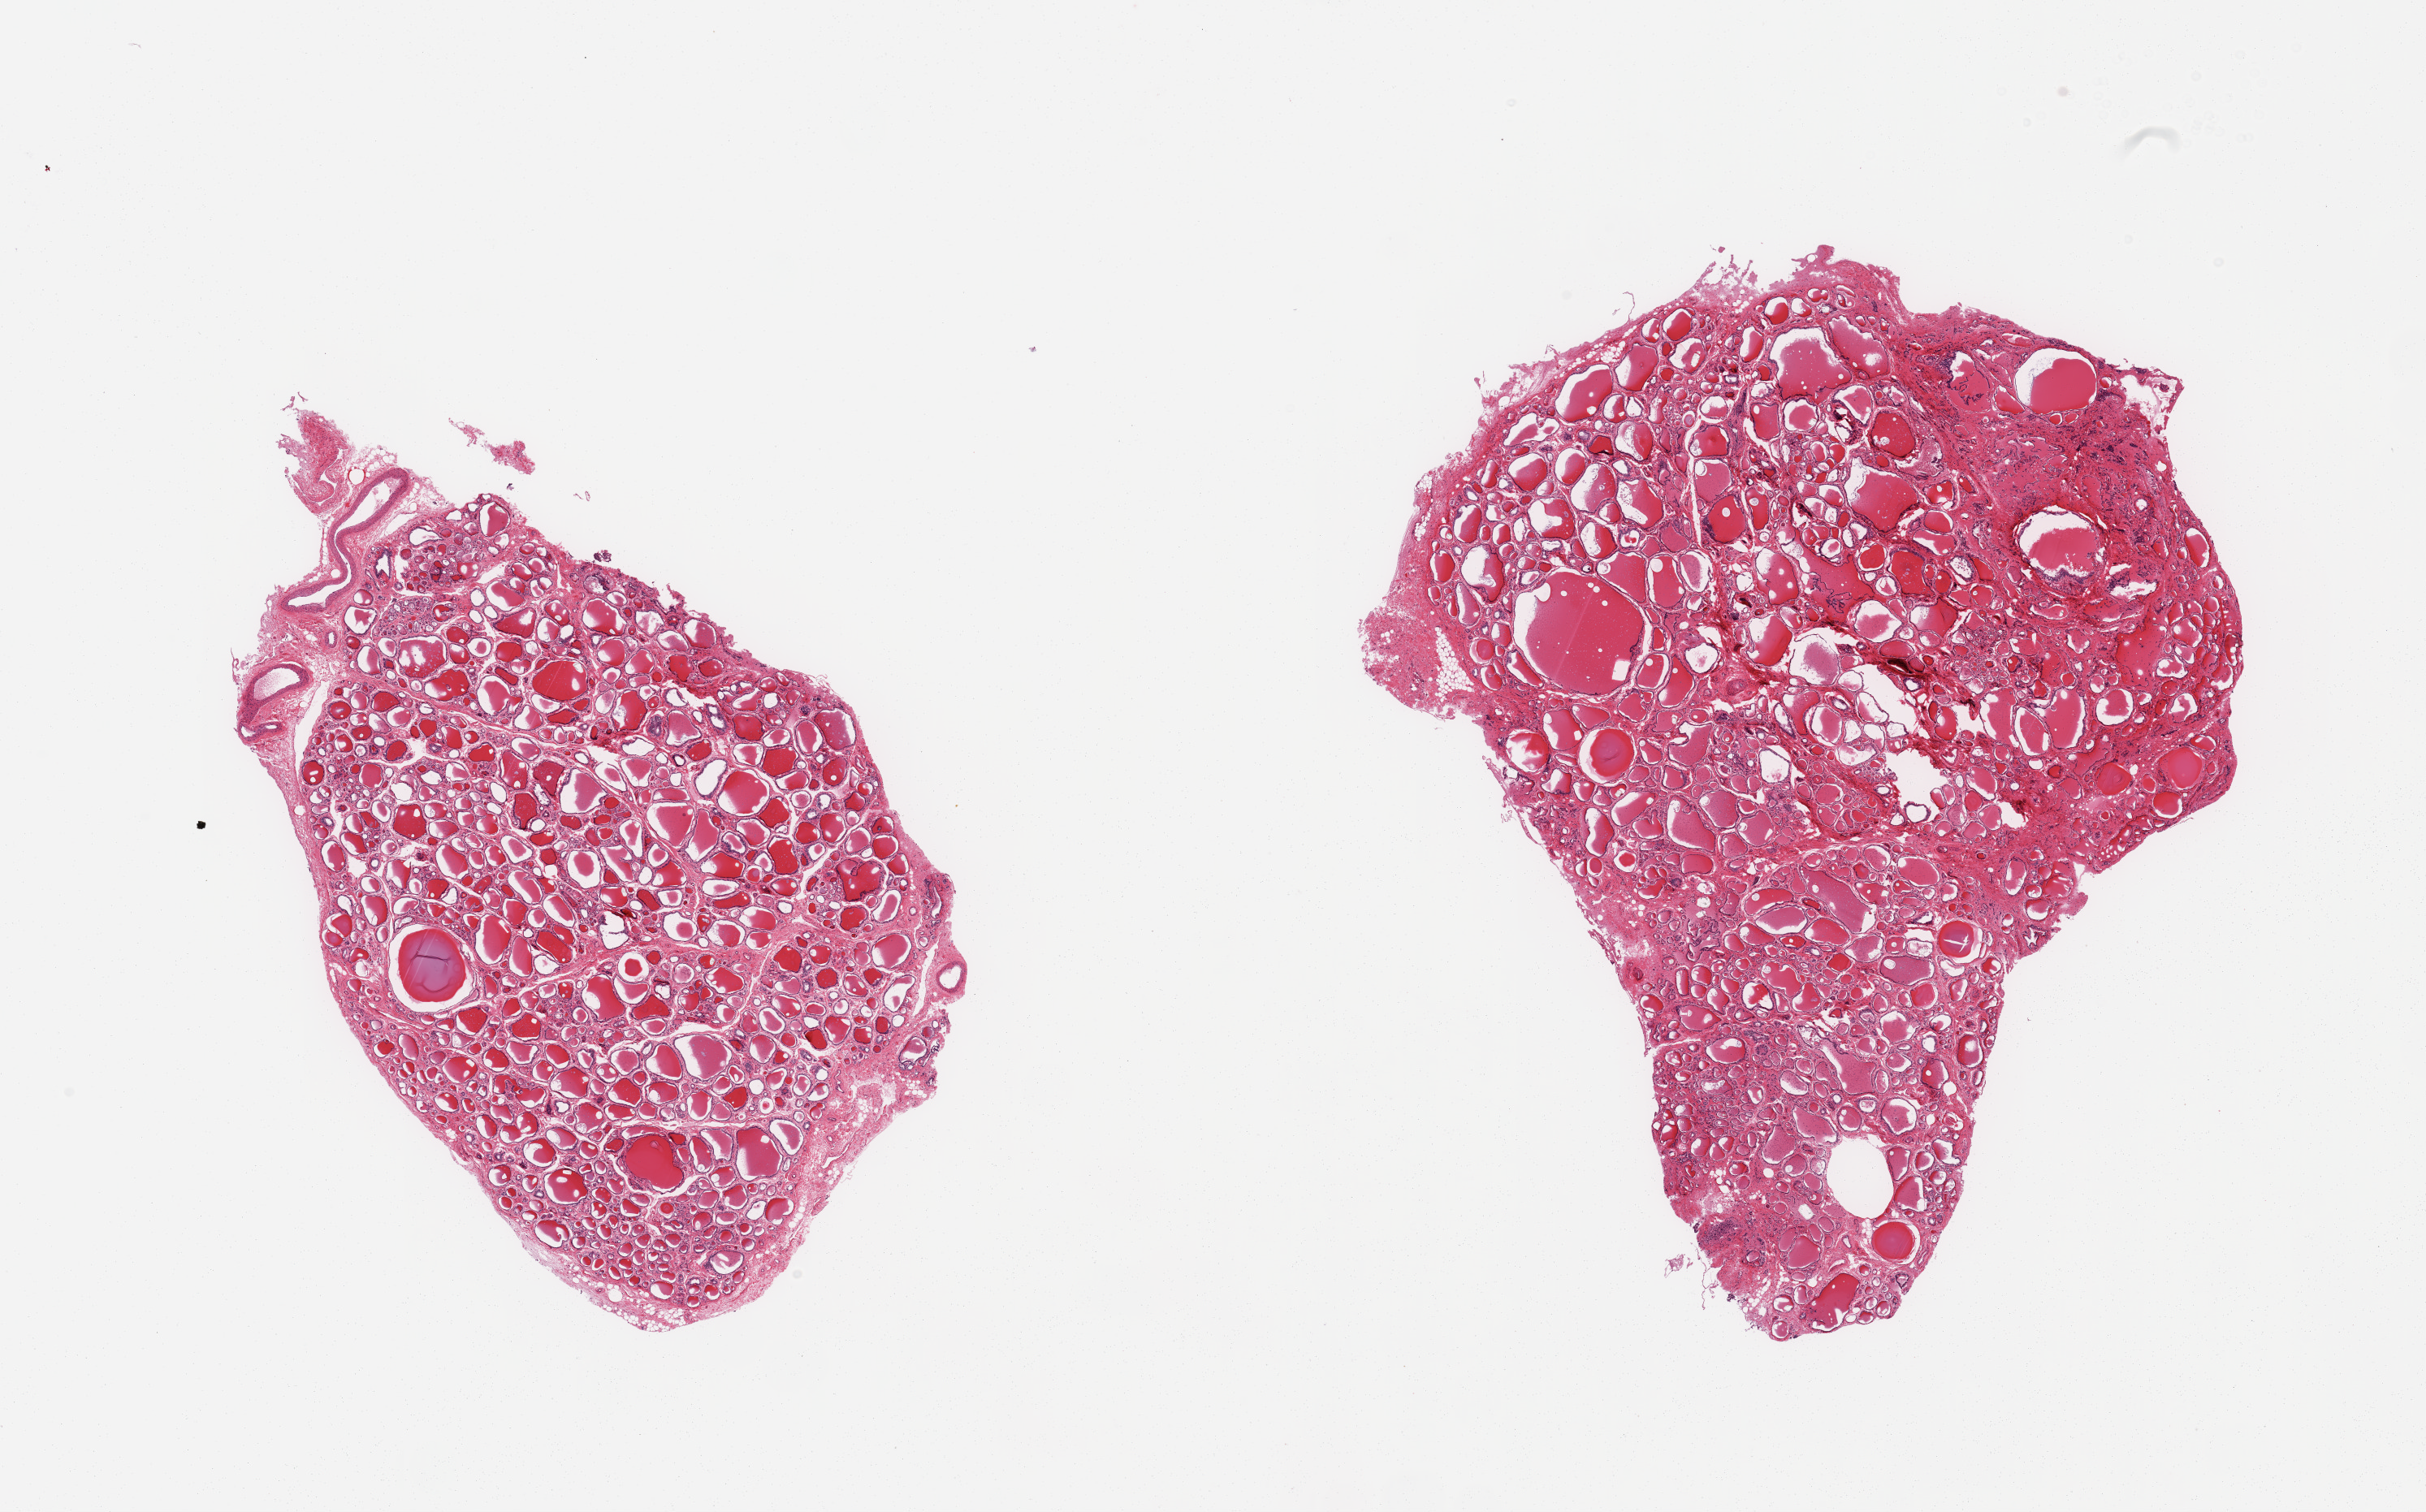
Digitized hematoxylin and eosin (H&E)-stained section, brightfield, shown as a low-resolution overview of the whole scanned area (about 23.6 x 14.7 mm, slide scanned at 20x); PAXgene-fixed paraffin-embedded (PFPE) section; sampled site (target tissue): thyroid; donor tissue sample. Donor: male.
• review note (as recorded): 2 pieces; blood vessels at 1 pole